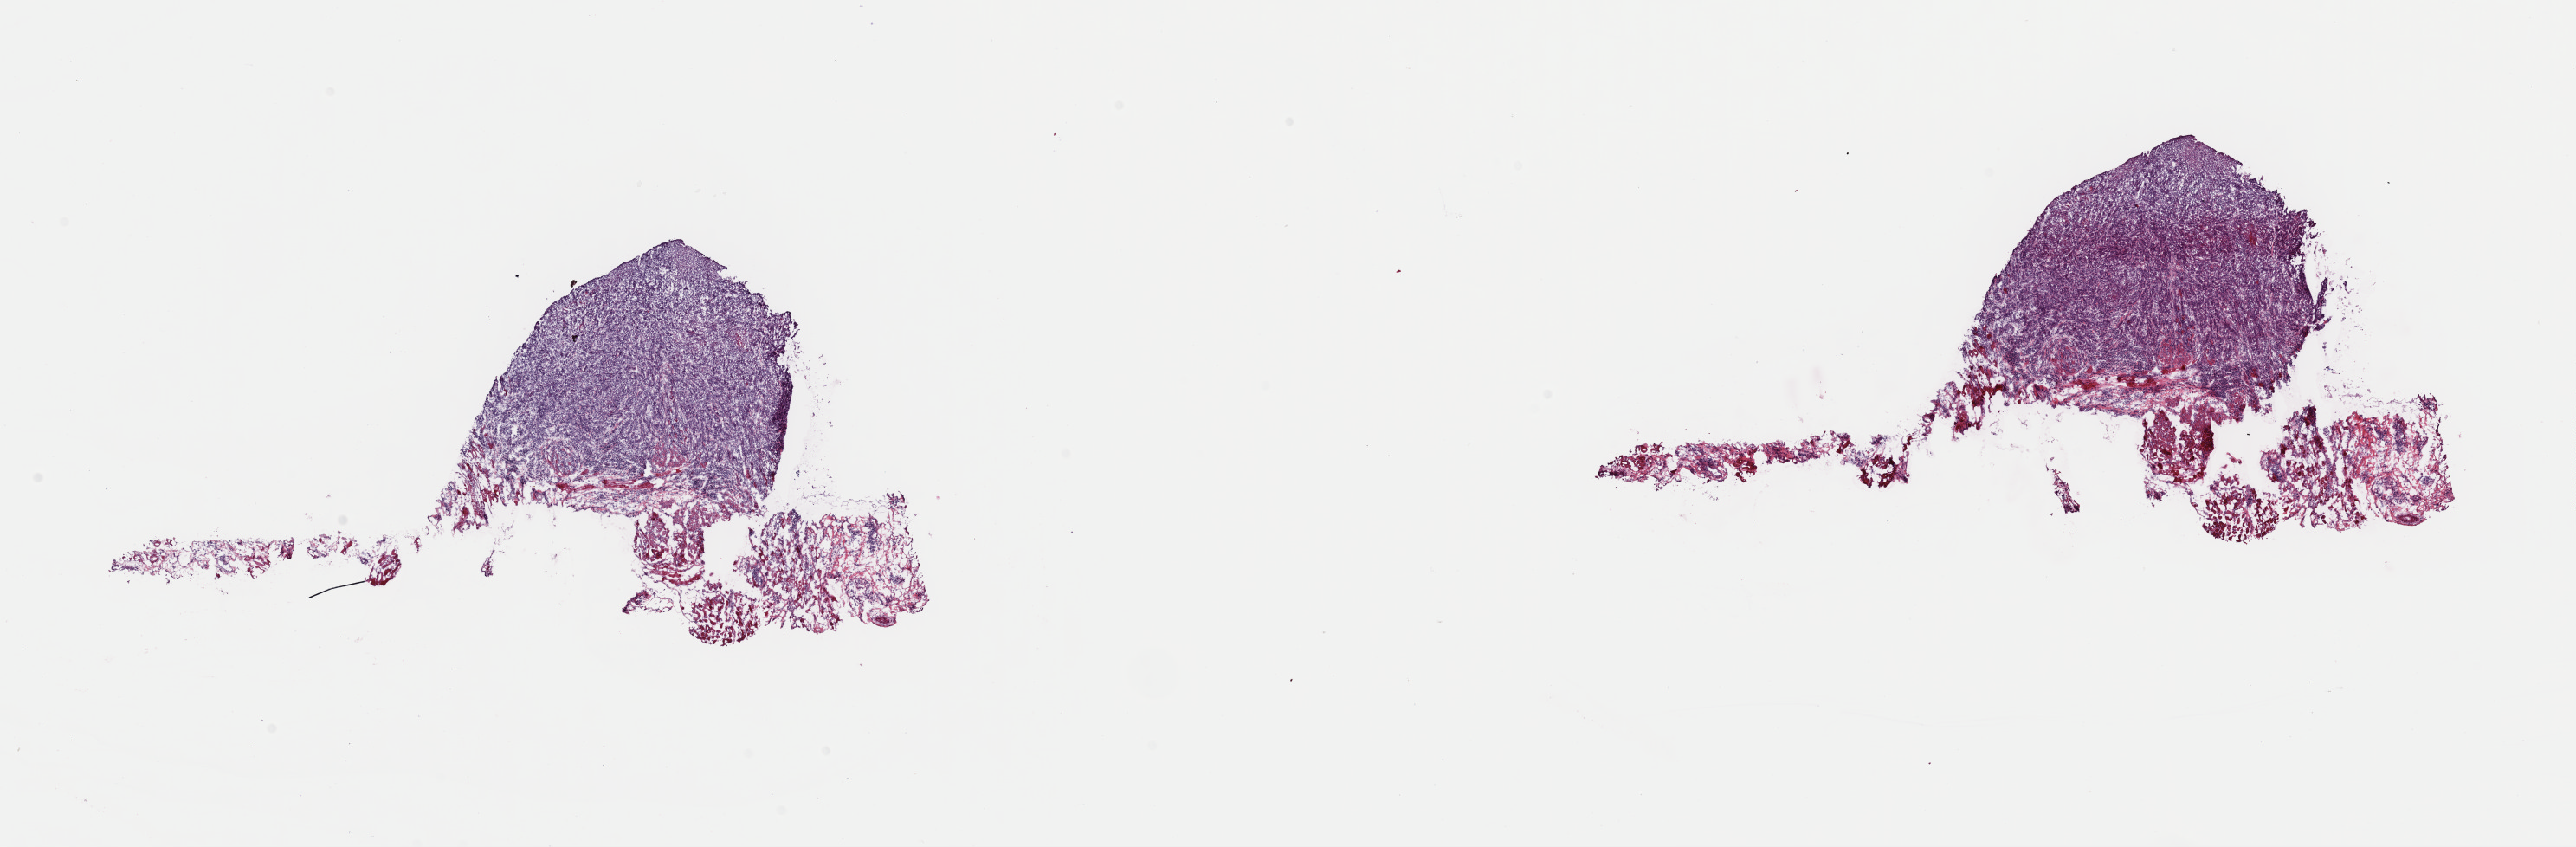
Hematoxylin and eosin (H&E) stained whole-slide image — a low-resolution overview of the entire scanned area, about 23.5 x 7.7 mm, frozen section, head and neck, primary tumour sample. Female patient; age at initial diagnosis 65 years. Histologic grade: G2 (moderately differentiated). Slide review estimates, as recorded: tumour cells 70%, tumour nuclei 75%, normal cells 30%, stromal cells 0%, necrosis 0%. Inflammatory infiltration, as recorded: lymphocyte infiltration 8%, monocyte infiltration 0%, neutrophil infiltration 0%.
Pathologic diagnosis: Squamous cell carcinoma, NOS (mouth, NOS). Lymph nodes positive (case pathology): 1 of 17 examined. AJCC pathologic stage: III (7th edition).